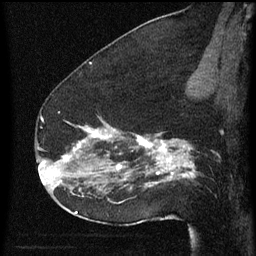
Breast MRI (dynamic contrast-enhanced), one sagittal slice; slice 39 of 60 in the series (ordered by position); dynamic contrast-enhanced series, image 2 of 3 at this slice position (ordered by acquisition); 1.5 T; TE 4.2 ms, TR 8 ms; 256 × 256 image matrix. Female patient, age 52 years.
Annotated regions visible in this slice (semi-automatic segmentation, software-assisted and operator-edited):
- analysis volume of interest (the breast-tissue region the enhancement analysis was run in; not a lesion): bounding box <54,112,178,207> (left, top, right, bottom; pixels)
- tumour enhancement mask (voxels above the 70 % enhancement threshold inside the analysis volume of interest): <65,128,178,187>